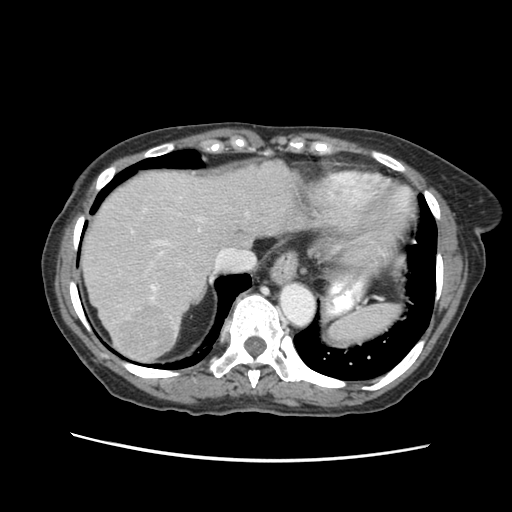
Contrast-enhanced abdominal CT (liver protocol), one axial slice; slice 48 of 63 in the series (ordered by position); reconstruction kernel STANDARD; 120 kVp; soft-tissue window (W 400 / L 40 HU); 512 × 512 image matrix. From the clinical record (not read from this slice): diagnosis: hepatocellular carcinoma (patient treated with transarterial chemoembolisation; whether this scan precedes or follows treatment is not stated here); TNM stage (as recorded): Stage-I; Child-Pugh class: B; tumour nodularity: uninodular.
Structures marked on this image (semi-automatic segmentation, software-assisted and operator-edited):
- liver parenchyma outside the tumour (the mass and vessels are separate outlines, so this box may not span the whole liver): bounding box [x1, y1, x2, y2] px = [80, 160, 303, 360]
- mass: [115, 305, 176, 358]
- liver vessels: [130, 208, 156, 300]